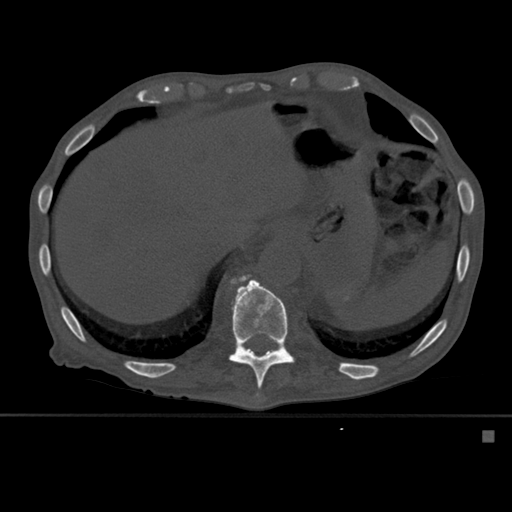
CT including the spine, one axial slice. Position 295 of 527 along the scan axis. Bone window (W 1800 / L 400 HU). 1.5 mm slice thickness. 512 × 512 image matrix. Patient: male, 78 years. Case-level facts recorded for this patient, not image findings: primary cancer: prostate.
Outlined on this slice (semi-automatically segmented with operator editing):
- T11 vertebra: bounding box (x1, y1, x2, y2) in pixels: (228, 275, 295, 398)